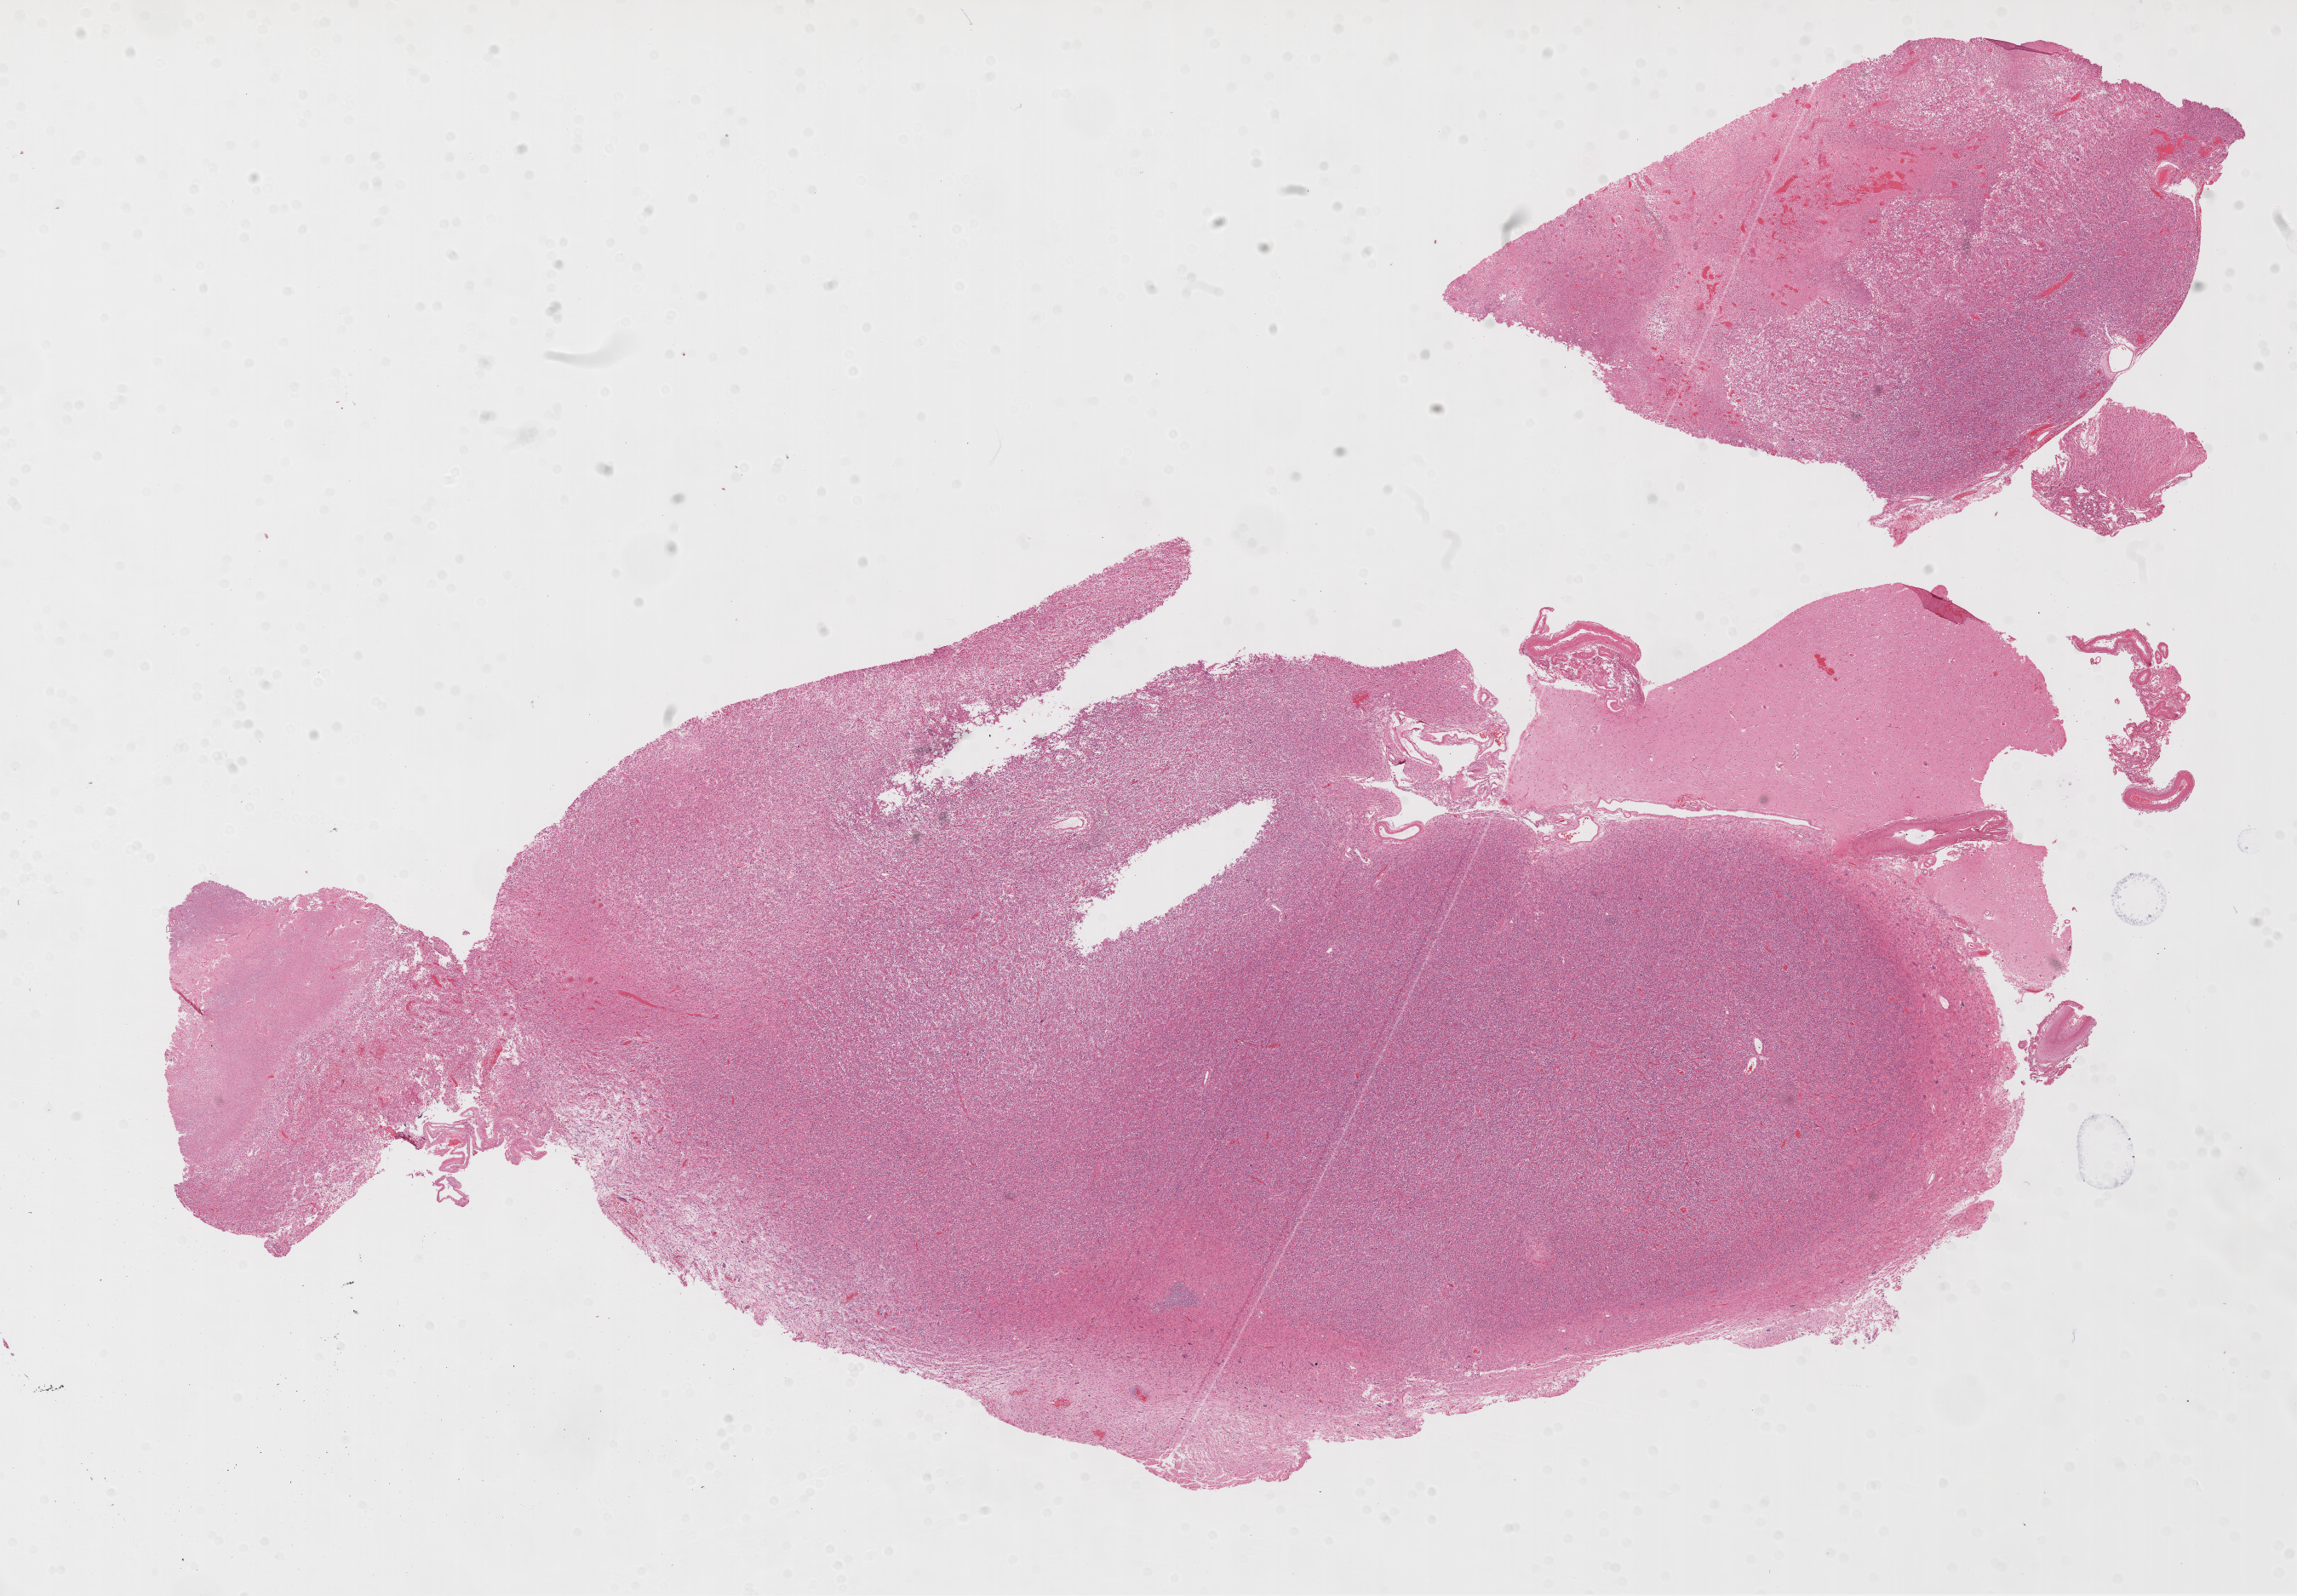
Whole-slide histology image, H&E-stained — shown as a low-resolution overview of the whole scanned area (about 21.8 x 15.1 mm, from a 20x scan), formalin-fixed paraffin-embedded (FFPE) diagnostic section, brain, primary tumour sample. Male, age 68 years at initial diagnosis.
Pathologic diagnosis: Glioblastoma.